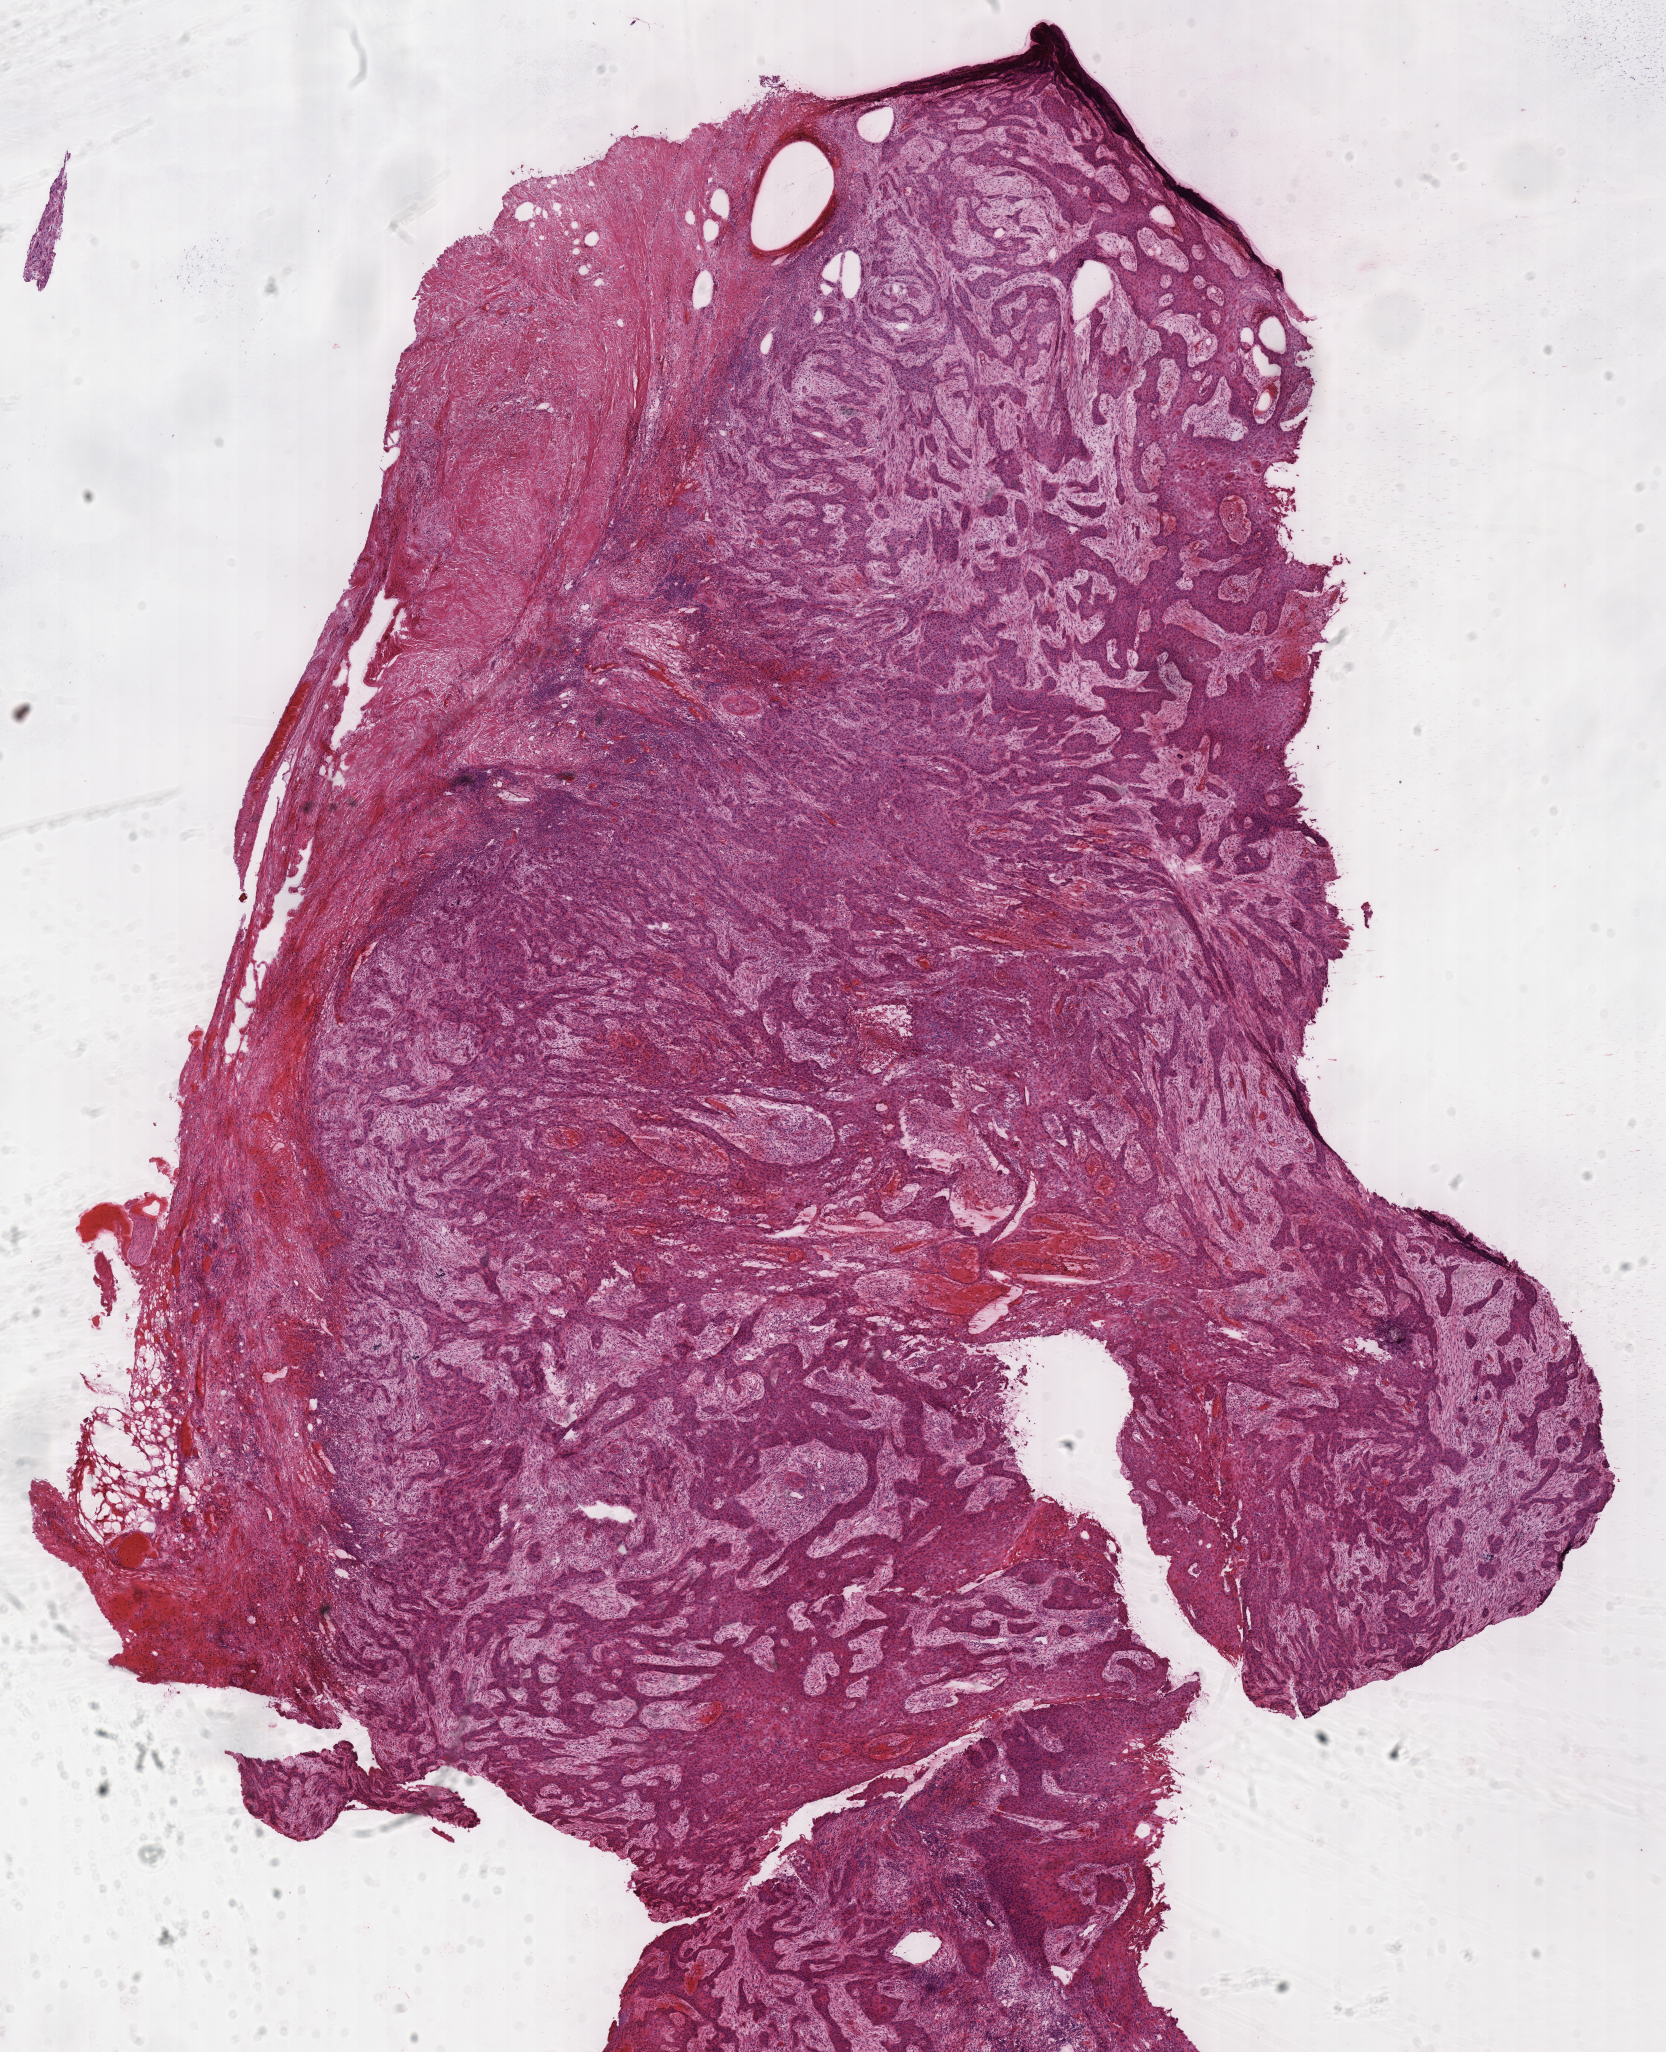
H&E-stained whole-slide image, low-resolution overview of the scanned area, about 13.1 x 16.2 mm. Frozen section from the top of the tissue portion. Primary tumour sample from the head and neck. Patient: male, age at initial diagnosis 49 years. Pathologist review of this section (percent, as recorded): tumour cells 70%, tumour nuclei 60%.
Diagnosis: Squamous cell carcinoma, NOS (oropharynx, NOS).